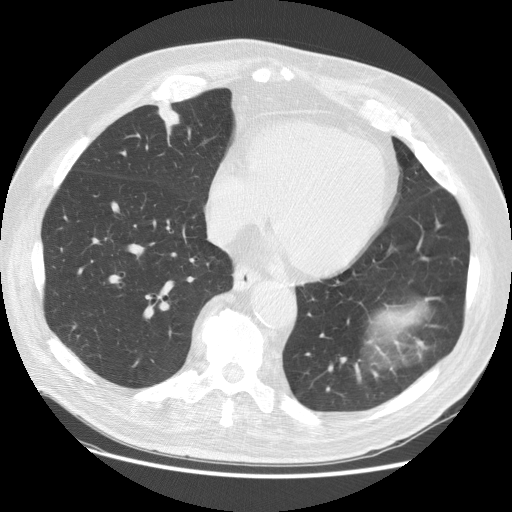
Low-dose screening chest CT, axial slice. First (baseline) screen. Lung window (W 1500 / L -600 HU). 2.5 mm slice thickness. Standard (soft-tissue) reconstruction kernel (STANDARD). Slice 90 of 129 in the series. 512 × 512 image matrix, field of view 397 × 397 mm. Male, age 74 years at enrolment.
Expert-annotated lung lesion, bounding box (x1, y1, x2, y2) in pixels: (148, 94, 186, 143). The exam's reader record, not a measurement of the box and not confirmed to be the same lesion: non-calcified nodule or mass ≥4 mm, right middle lobe, 24 × 24 mm, spiculated (stellate) margins, soft tissue attenuation. Official screen result: positive, change unspecified: nodule(s) >= 4 mm or enlarging nodule(s), mass(es), or other non-specific abnormalities suspicious for lung cancer. Participant outcome: lung cancer diagnosed 296 days after this screen — papillary adenocarcinoma, NOS, right middle lobe, well differentiated (G1), stage IA (AJCC 6th edition), 20 mm at pathology.